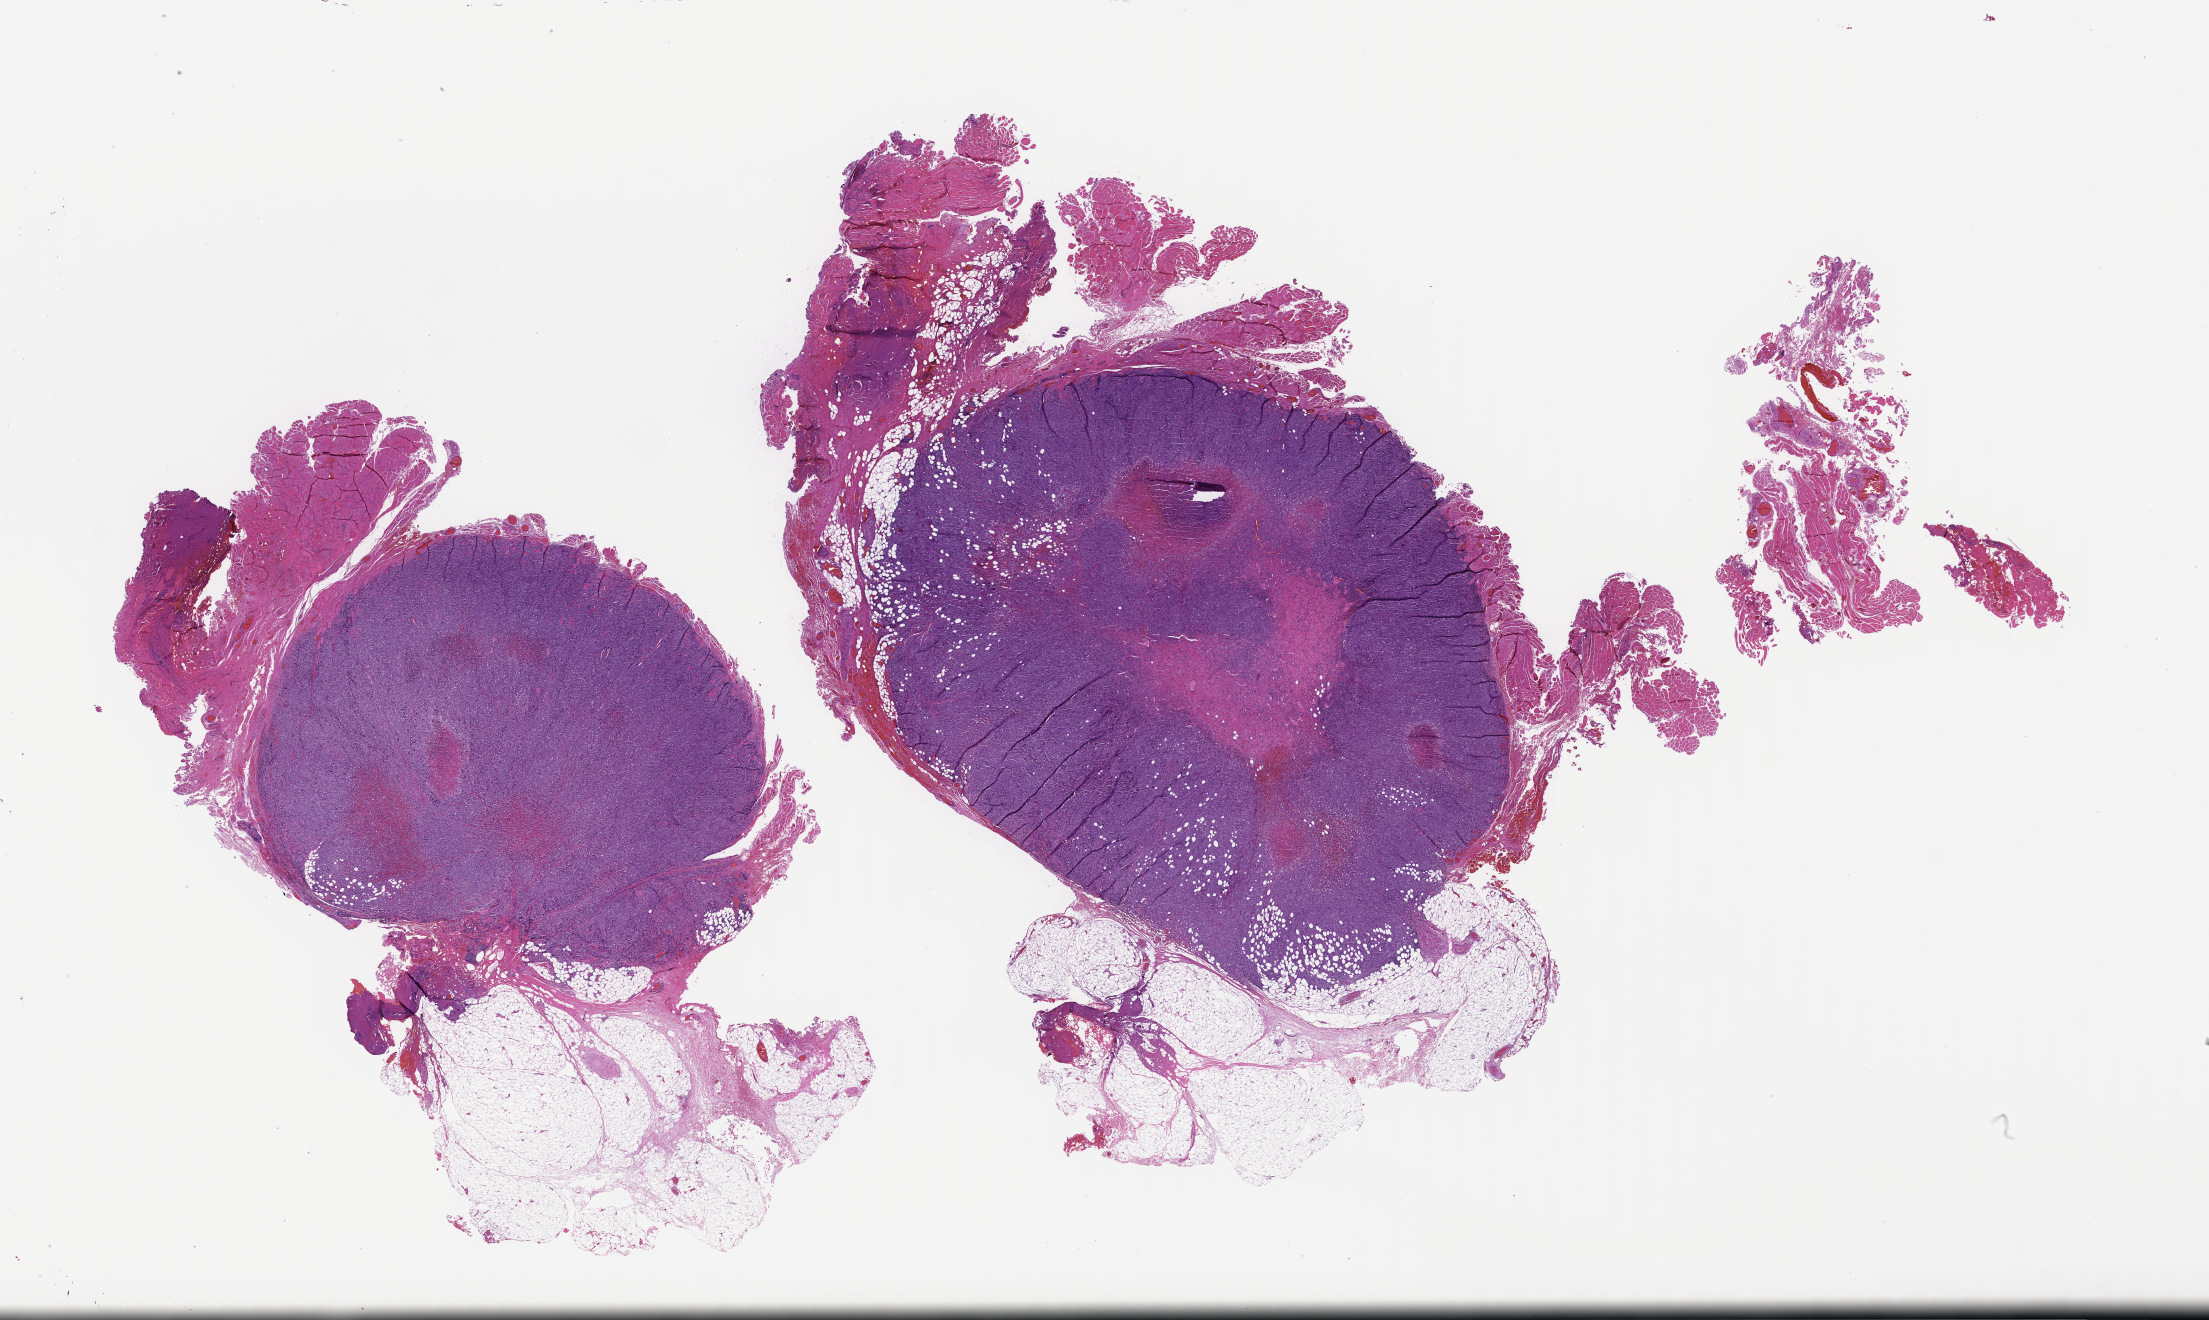
Digitized H&E-stained section, a low-resolution overview of the entire scanned area, about 35.7 x 21.3 mm. FFPE section. Archival tissue. Male patient.
This section: metastatic tumor tissue. Patient diagnosis (primary): Melanoma.